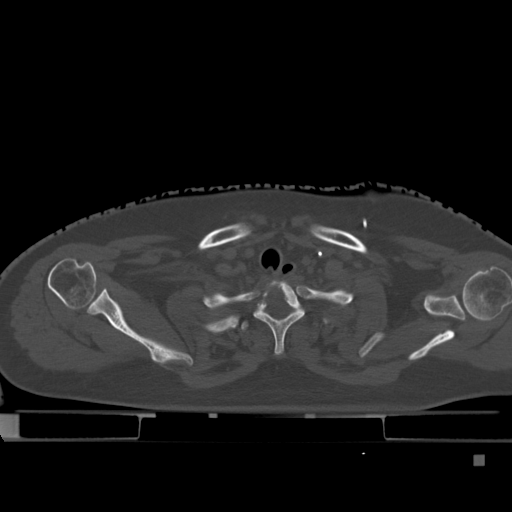
CT including the spine, one axial slice. Position 369 of 495 along the scan axis. Bone window (W 1800 / L 400 HU). 512 × 512 image matrix, field of view 404 × 404 mm. Female patient, age 33 years. Case-level facts recorded for this patient, not image findings: primary cancer: breast; vertebrae with lytic lesions (as recorded): T1.
Outlined on this slice (semi-automatically segmented with operator editing):
- T1 vertebra: bounding box <254,282,304,355> (left, top, right, bottom; pixels)
- T2 vertebra: <241,307,335,331>